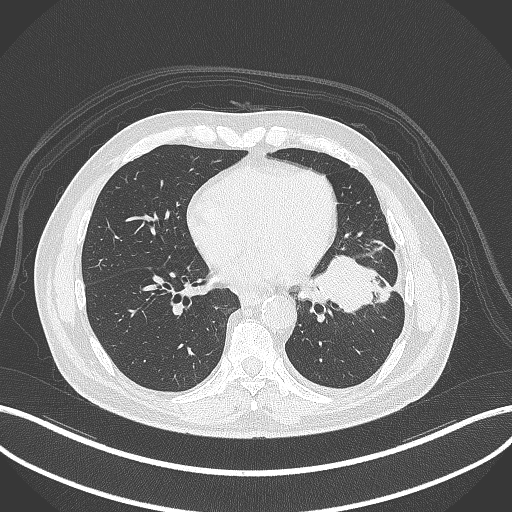
Chest CT, one axial slice; slice 144 of 230 in the series (ordered by position); reconstruction kernel B70f; 120 kVp; lung window (W 1500 / L -600 HU); 1 mm slice thickness; 512 × 512 image matrix, field of view 400 × 400 mm. Patient: male, 68 years. From the clinical record (not read from this slice): clinical TNM (as recorded): T2b N0 M0.
Structures marked on this image (bounding box drawn by a radiologist):
- lung tumour (recorded histology: squamous cell carcinoma): bounding box <313,250,380,315> (left, top, right, bottom; pixels)